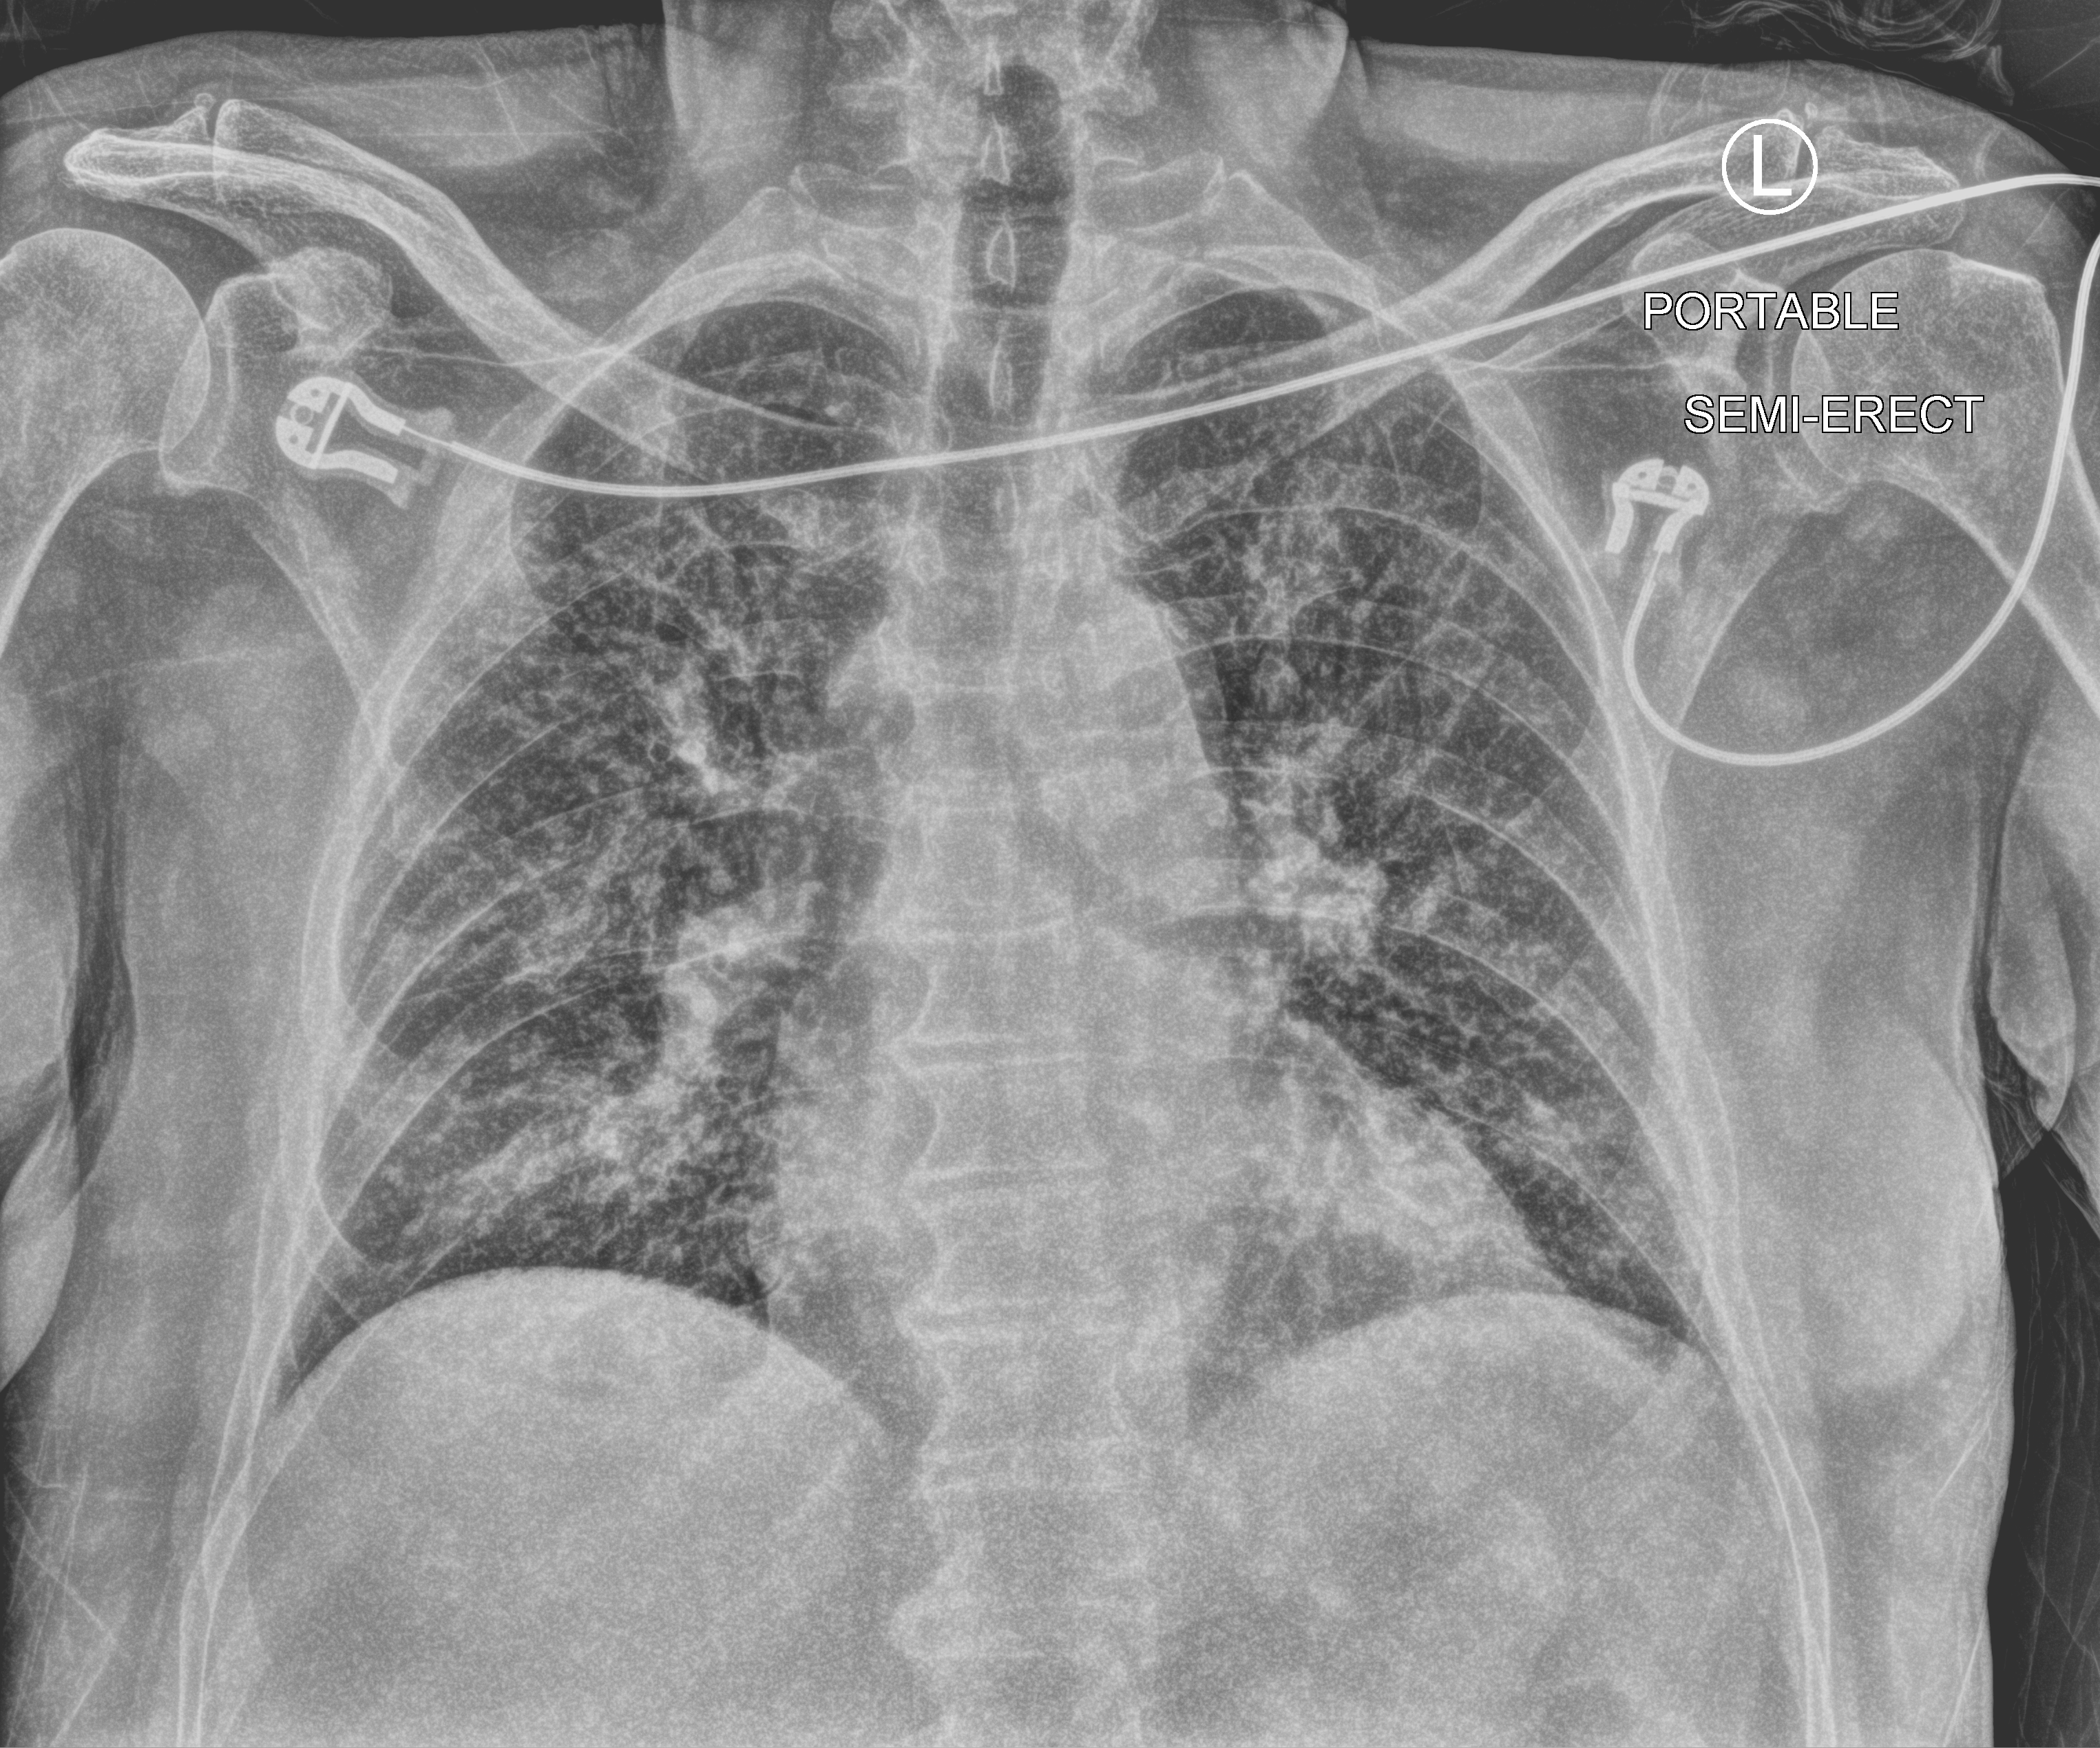
Chest X-ray (portable). Patient hospitalised with COVID-19; male, aged 75–90 years.
Admission-level facts for this patient (not findings on this image; timing relative to this image not recorded):
- admitted to intensive care during this hospital stay: yes
- mechanically ventilated during this hospital stay: yes
- other chronic lung disease (admission record): no